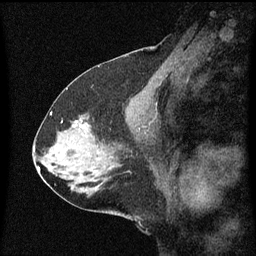
Breast MRI (dynamic contrast-enhanced), one sagittal slice. Slice 31 of 60 in the series (ordered by position). Dynamic contrast-enhanced series, image 2 of 3 at this slice position (ordered by acquisition). 1.5 T. TE 4.2 ms, TR 8.4 ms. 2 mm slice thickness. 256 × 256 image matrix, field of view 200 × 200 mm. Patient: female, 59 years.
Annotated regions visible in this slice (semi-automatic segmentation, software-assisted and operator-edited):
- analysis volume of interest (the breast-tissue region the enhancement analysis was run in; not a lesion): bounding box [x1, y1, x2, y2] px = [70, 116, 95, 137]
- tumour enhancement mask (voxels above the 70 % enhancement threshold inside the analysis volume of interest): [77, 120, 87, 127]